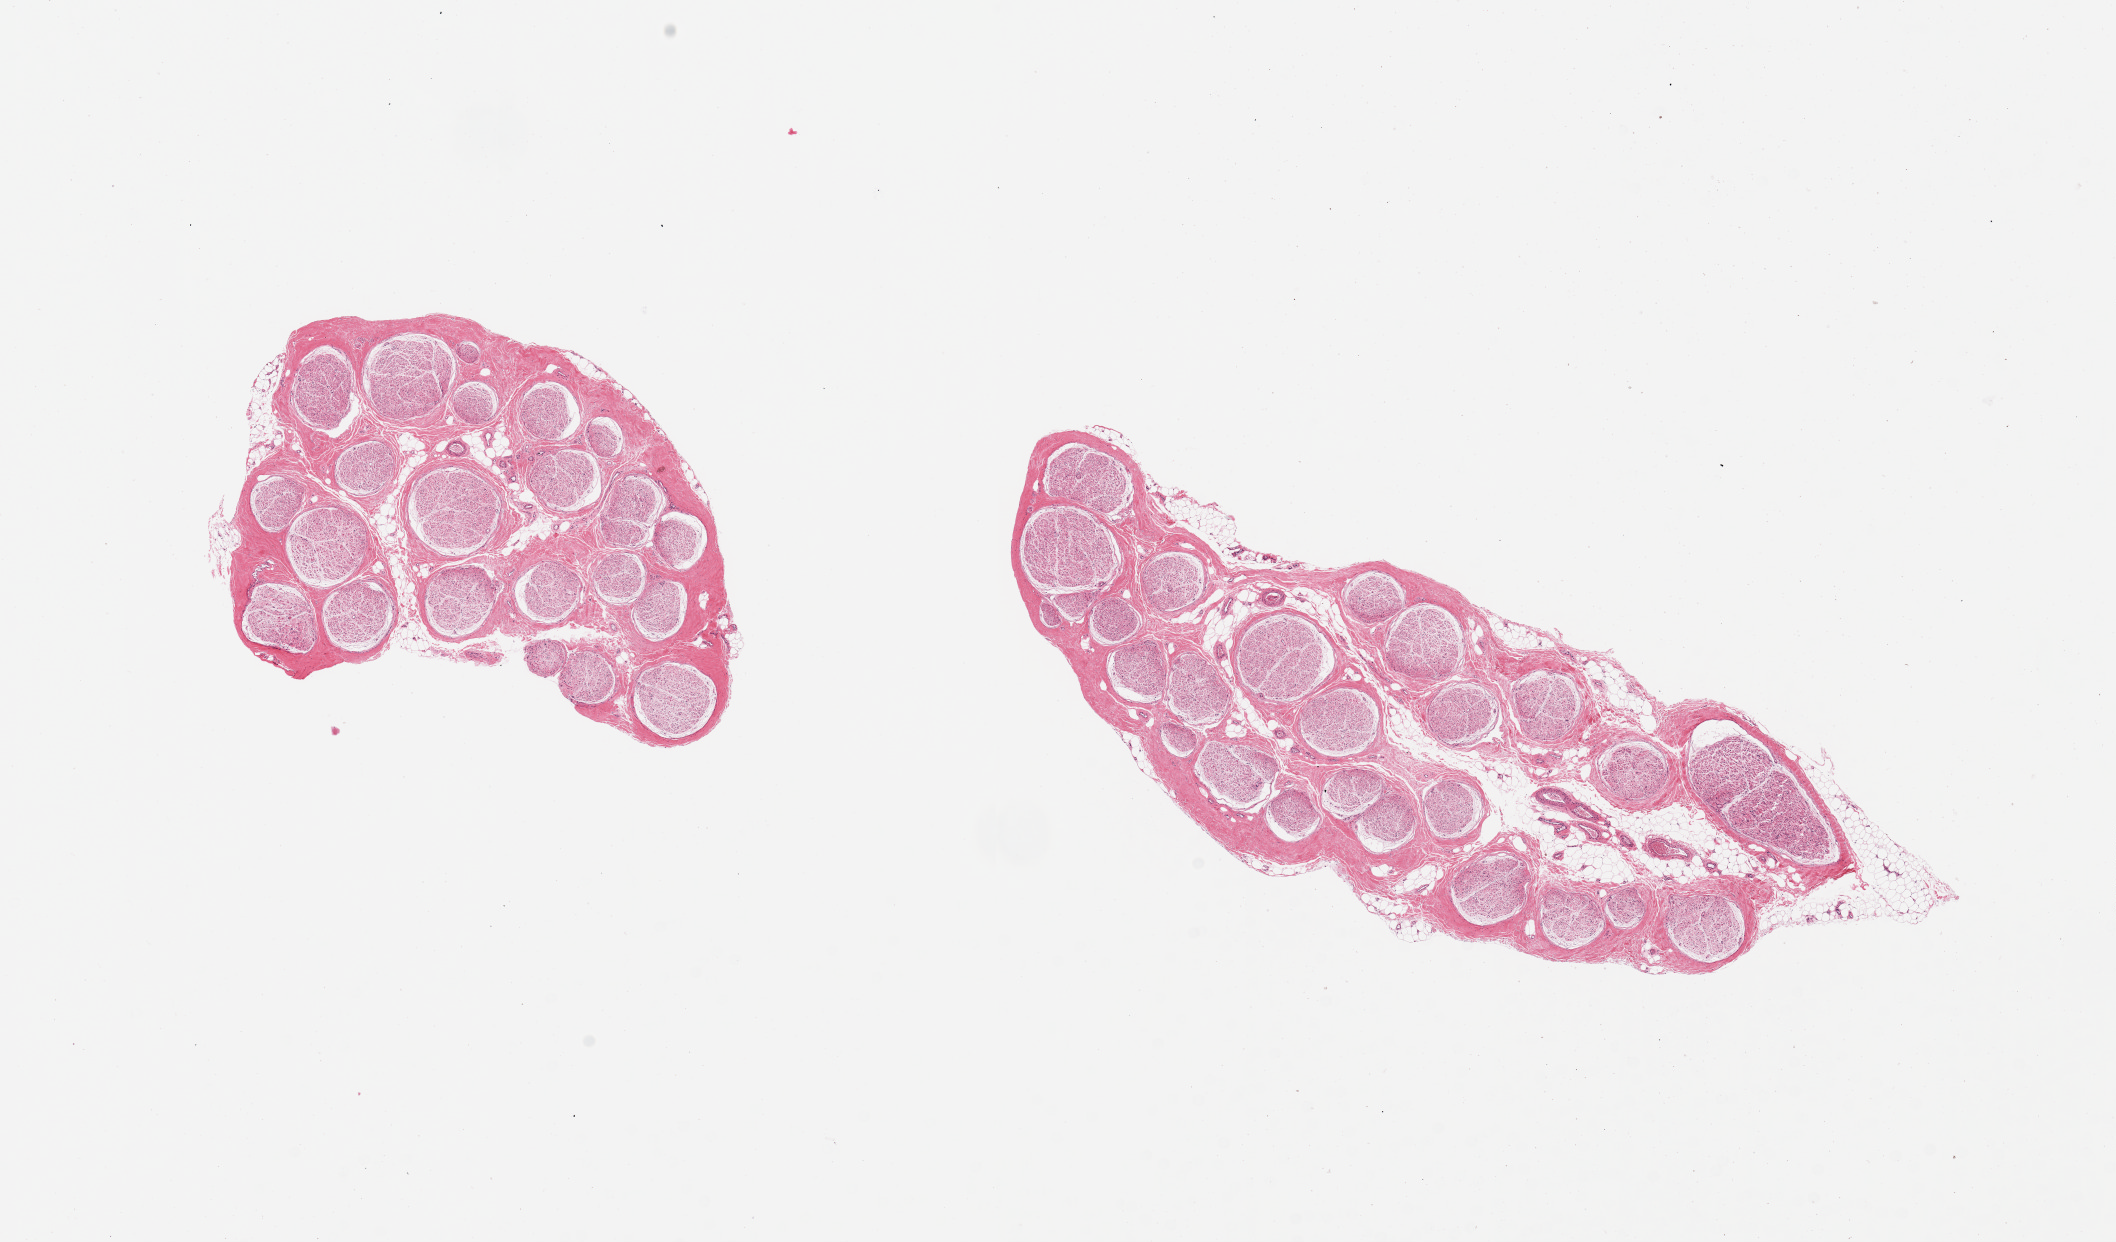
Digitized hematoxylin and eosin (H&E)-stained section — a low-resolution overview of the entire scanned area, about 16.7 x 9.8 mm (acquisition: 20x scan). PAXgene-fixed paraffin-embedded (PFPE) section. Target tissue: tibial nerve. Tissue donor sample. Donor sex: male.
Review note (as recorded): 2 pieces, larger piece has ~10% adipose tissue.